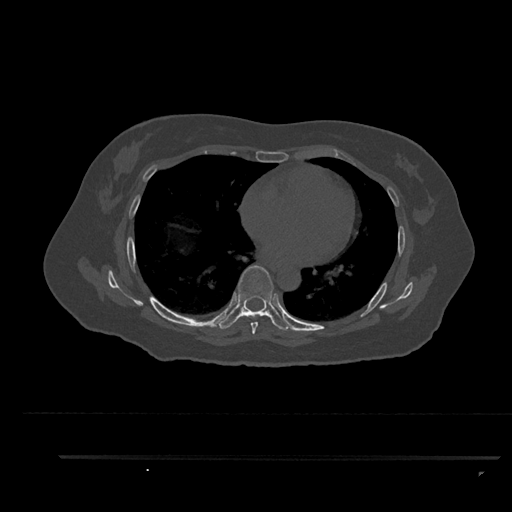
CT including the spine, one axial slice. Slice 524 of 797 in the series (ordered by position). Reconstruction kernel Br40s/3. 120 kVp. Bone window (W 1800 / L 400 HU). 0.5 mm slice thickness. 512 × 512 image matrix, field of view 408 × 408 mm. Patient: female, 44 years. Case-level facts recorded for this patient, not image findings: primary cancer: renal.
Annotated regions visible in this slice (semi-automatically segmented with operator editing):
- T6 vertebra: bounding box <250,316,259,335> (left, top, right, bottom; pixels)
- T7 vertebra: <218,265,291,331>